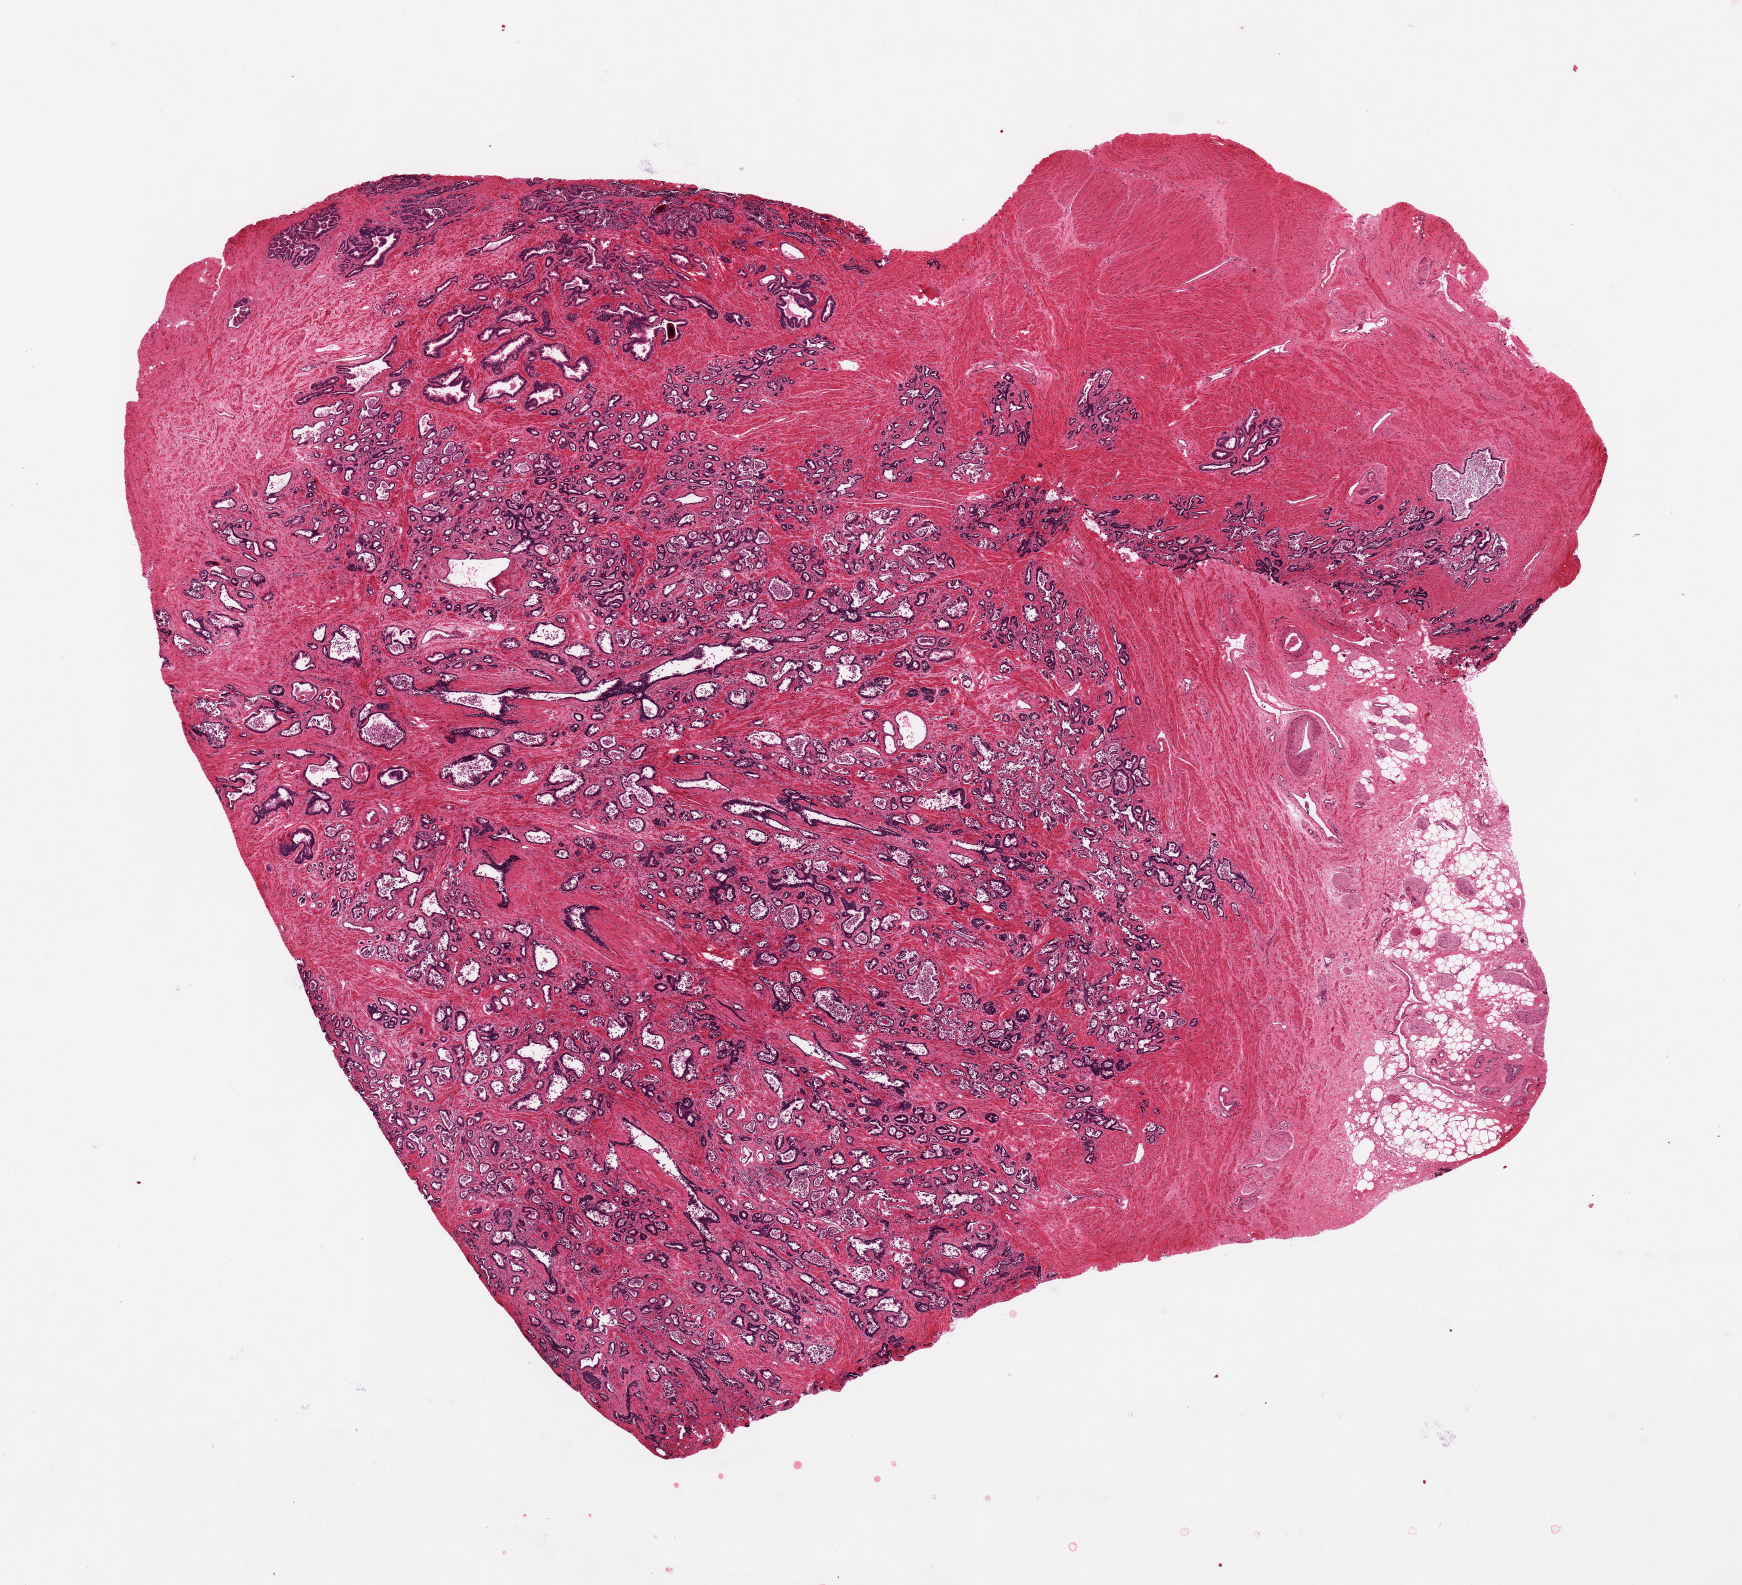
Whole-slide image, haematoxylin and eosin stain, shown as a low-resolution overview of the whole scanned area (about 13.8 x 12.5 mm); PAXgene-fixed, paraffin-embedded tissue; target tissue: prostate; donor tissue sample. Male donor.
* pathologist's review note for this sample: 10 x 11 mm